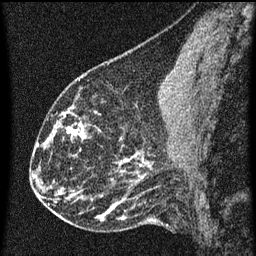
Breast MRI (dynamic contrast-enhanced), one sagittal slice; position 27 of 60 along the scan axis; dynamic contrast-enhanced series, image 2 of 3 at this slice position (ordered by acquisition); 1.5 T; TE 4.2 ms, TR 8 ms; 2 mm slice thickness; 256 × 256 image matrix, field of view 180 × 180 mm. Female patient, age 43 years.
Structures marked on this image (semi-automatically segmented with operator editing):
- analysis volume of interest (the breast-tissue region the enhancement analysis was run in; not a lesion): bounding box [x1, y1, x2, y2] px = [55, 104, 101, 151]
- tumour enhancement mask (voxels above the 70 % enhancement threshold inside the analysis volume of interest): [64, 114, 86, 139]